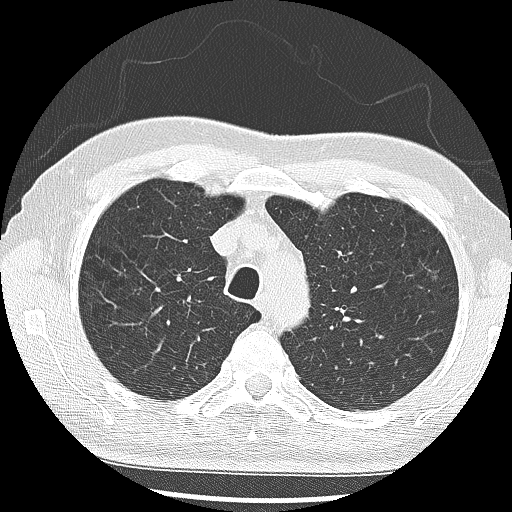
Low-dose screening chest CT, one axial slice; slice 217 of 285 in the series (ordered by position); reconstruction kernel LUNG; lung window (W 1500 / L -600 HU); 512 × 512 image matrix, field of view 340 × 340 mm.
Structures marked on this image (expert manual segmentation):
- lesion 1 (tumor, upper lobe of left lung): bounding box [x1, y1, x2, y2] px = [432, 271, 439, 281]